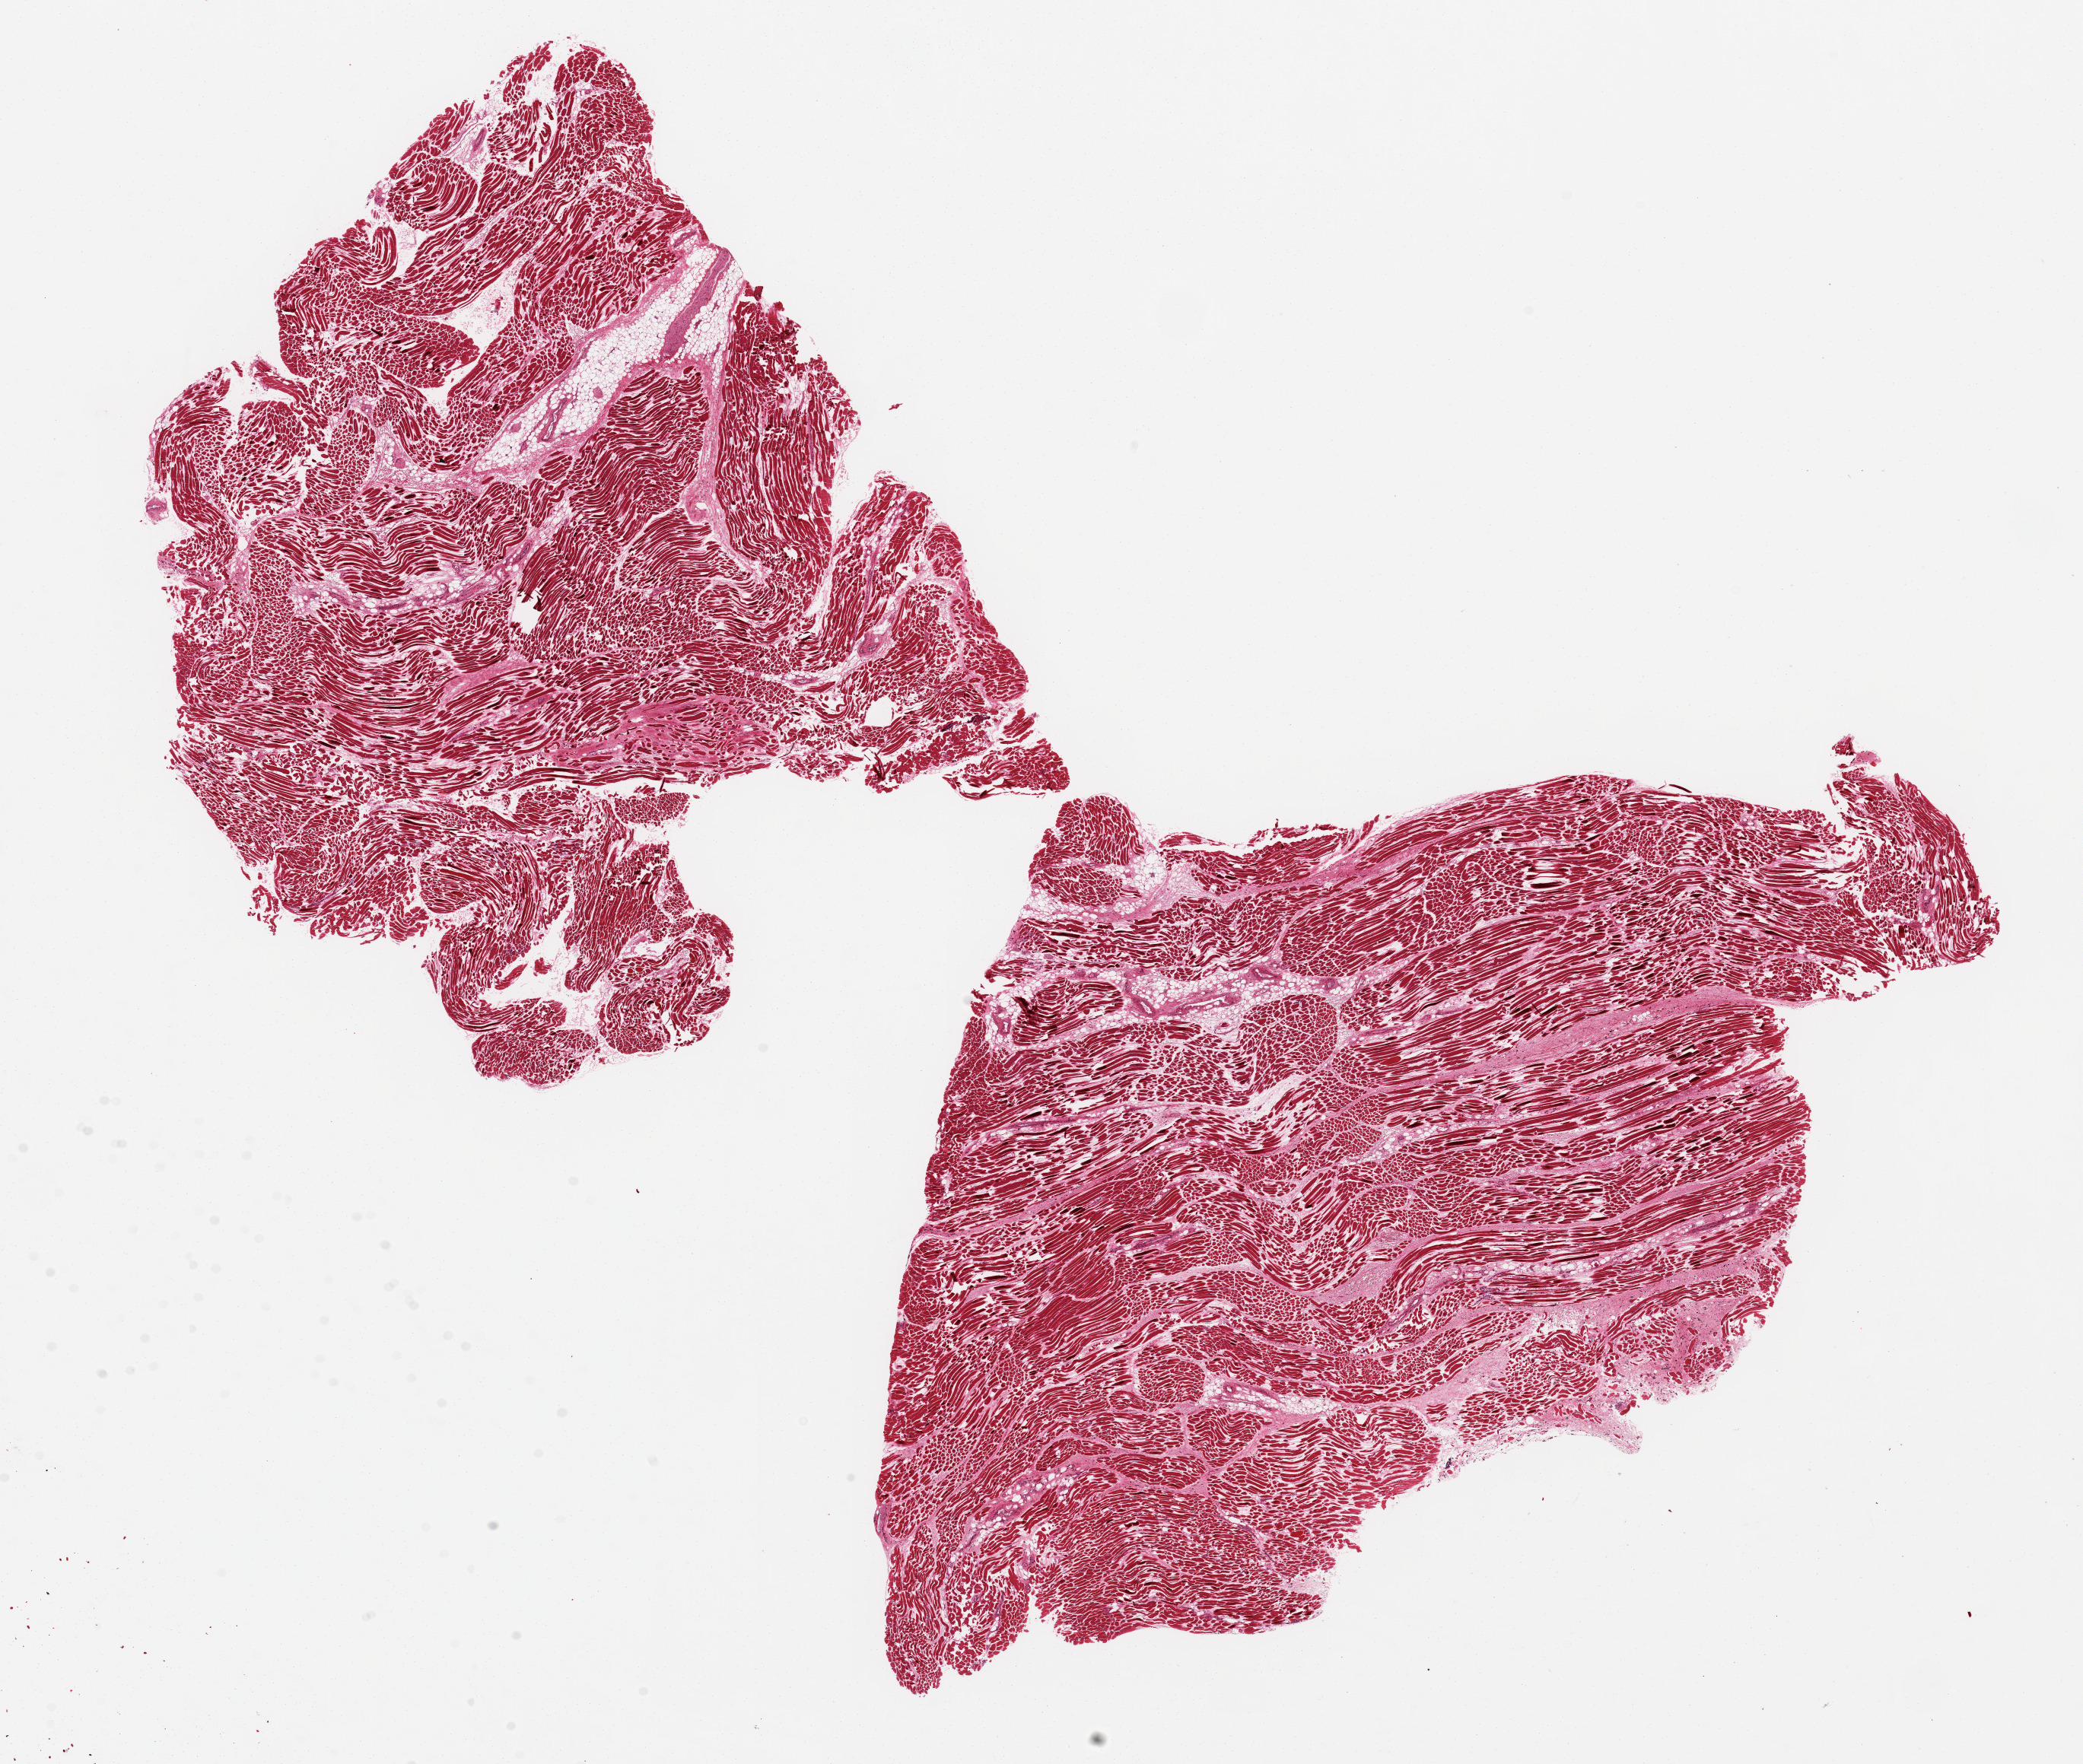
Digitized hematoxylin and eosin (H&E)-stained section — a low-resolution overview of the entire scanned area, about 21.7 x 18.3 mm (acquisition: 20x scan), PAXgene-fixed, paraffin-embedded tissue, section of skeletal muscle (target tissue), donor tissue sample. Donor sex: female.
Review note (as recorded): 2 ~9x8mm aliquots, about 30% interspersed fat.